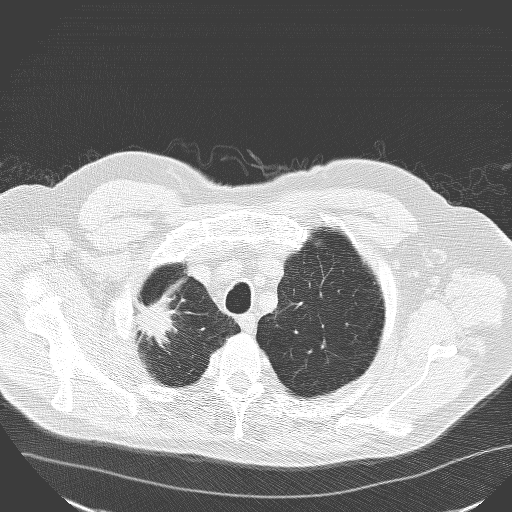
Low-dose screening chest CT, axial slice, baseline annual screen, lung window (W 1500 / L -600 HU), 3.2 mm slice thickness, lung (sharp) reconstruction kernel (D). Male participant, aged 71 years at enrolment.
Lesion marked by an expert reader, box from (x=118, y=287) to (x=189, y=360) px. Screening reader's record for this exam (one nodule recorded; not confirmed to be the boxed lesion): non-calcified nodule or mass ≥4 mm, right upper lobe, 30 × 25 mm, spiculated (stellate) margins, soft tissue attenuation. Lung cancer was diagnosed 182 days after this screen: squamous cell carcinoma, NOS, right upper lobe, poorly differentiated (G3), stage IA (AJCC 6th edition), 30 mm at pathology.